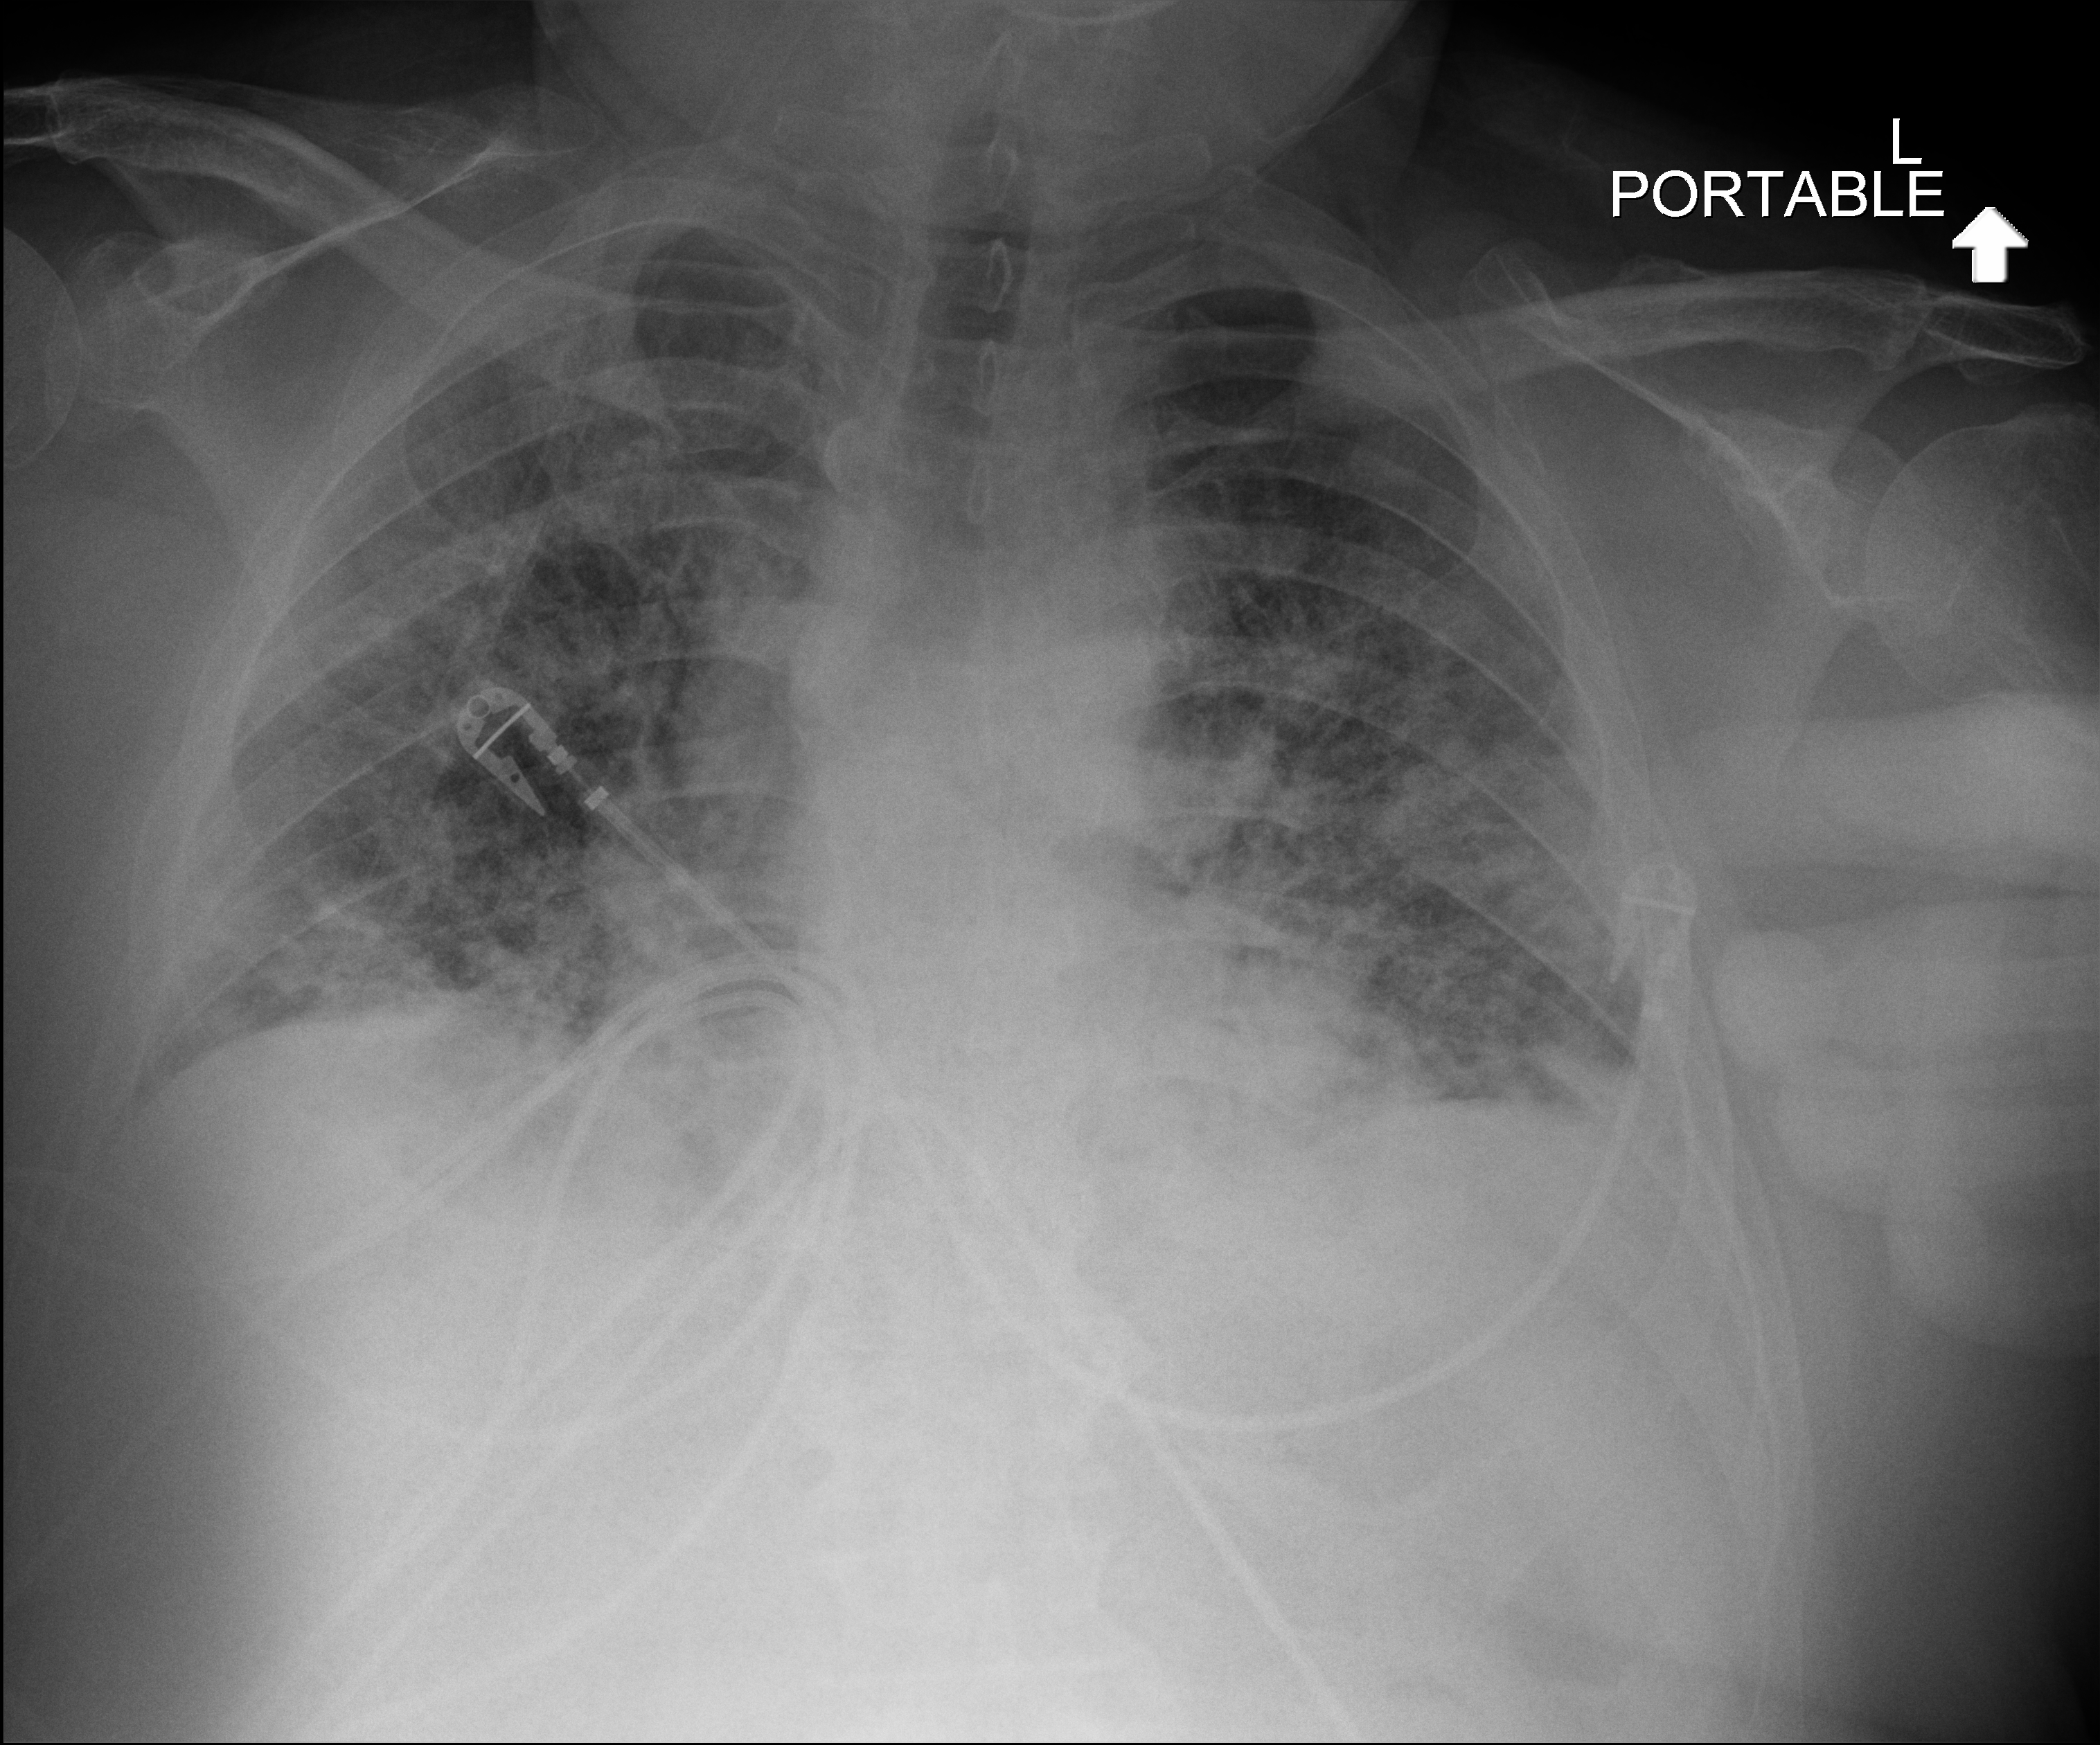
Chest X-ray; anteroposterior (AP) projection. Patient hospitalised with COVID-19; male, aged 18–59 years.
From the hospital-stay record, not from the radiograph (when in the stay this image was taken is not recorded): length of hospital stay: 25 days; hypertension (admission record): yes; mechanically ventilated during this hospital stay: no.